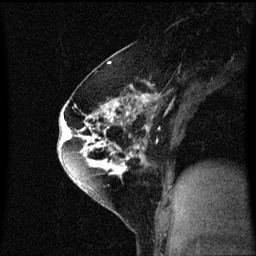
Breast MRI (dynamic contrast-enhanced), one sagittal slice; position 35 of 60 along the scan axis; dynamic contrast-enhanced series, image 2 of 3 at this slice position (ordered by acquisition); 1.5 T; TE 4.2 ms, TR 8.4 ms; 2 mm slice thickness; 256 × 256 image matrix. Female patient, age 60 years.
Annotated regions visible in this slice (semi-automatically segmented with operator editing):
- analysis volume of interest (the breast-tissue region the enhancement analysis was run in; not a lesion): box from (x=64, y=70) to (x=149, y=195) px
- tumour enhancement mask (voxels above the 70 % enhancement threshold inside the analysis volume of interest): (x=64, y=84)–(x=149, y=187)